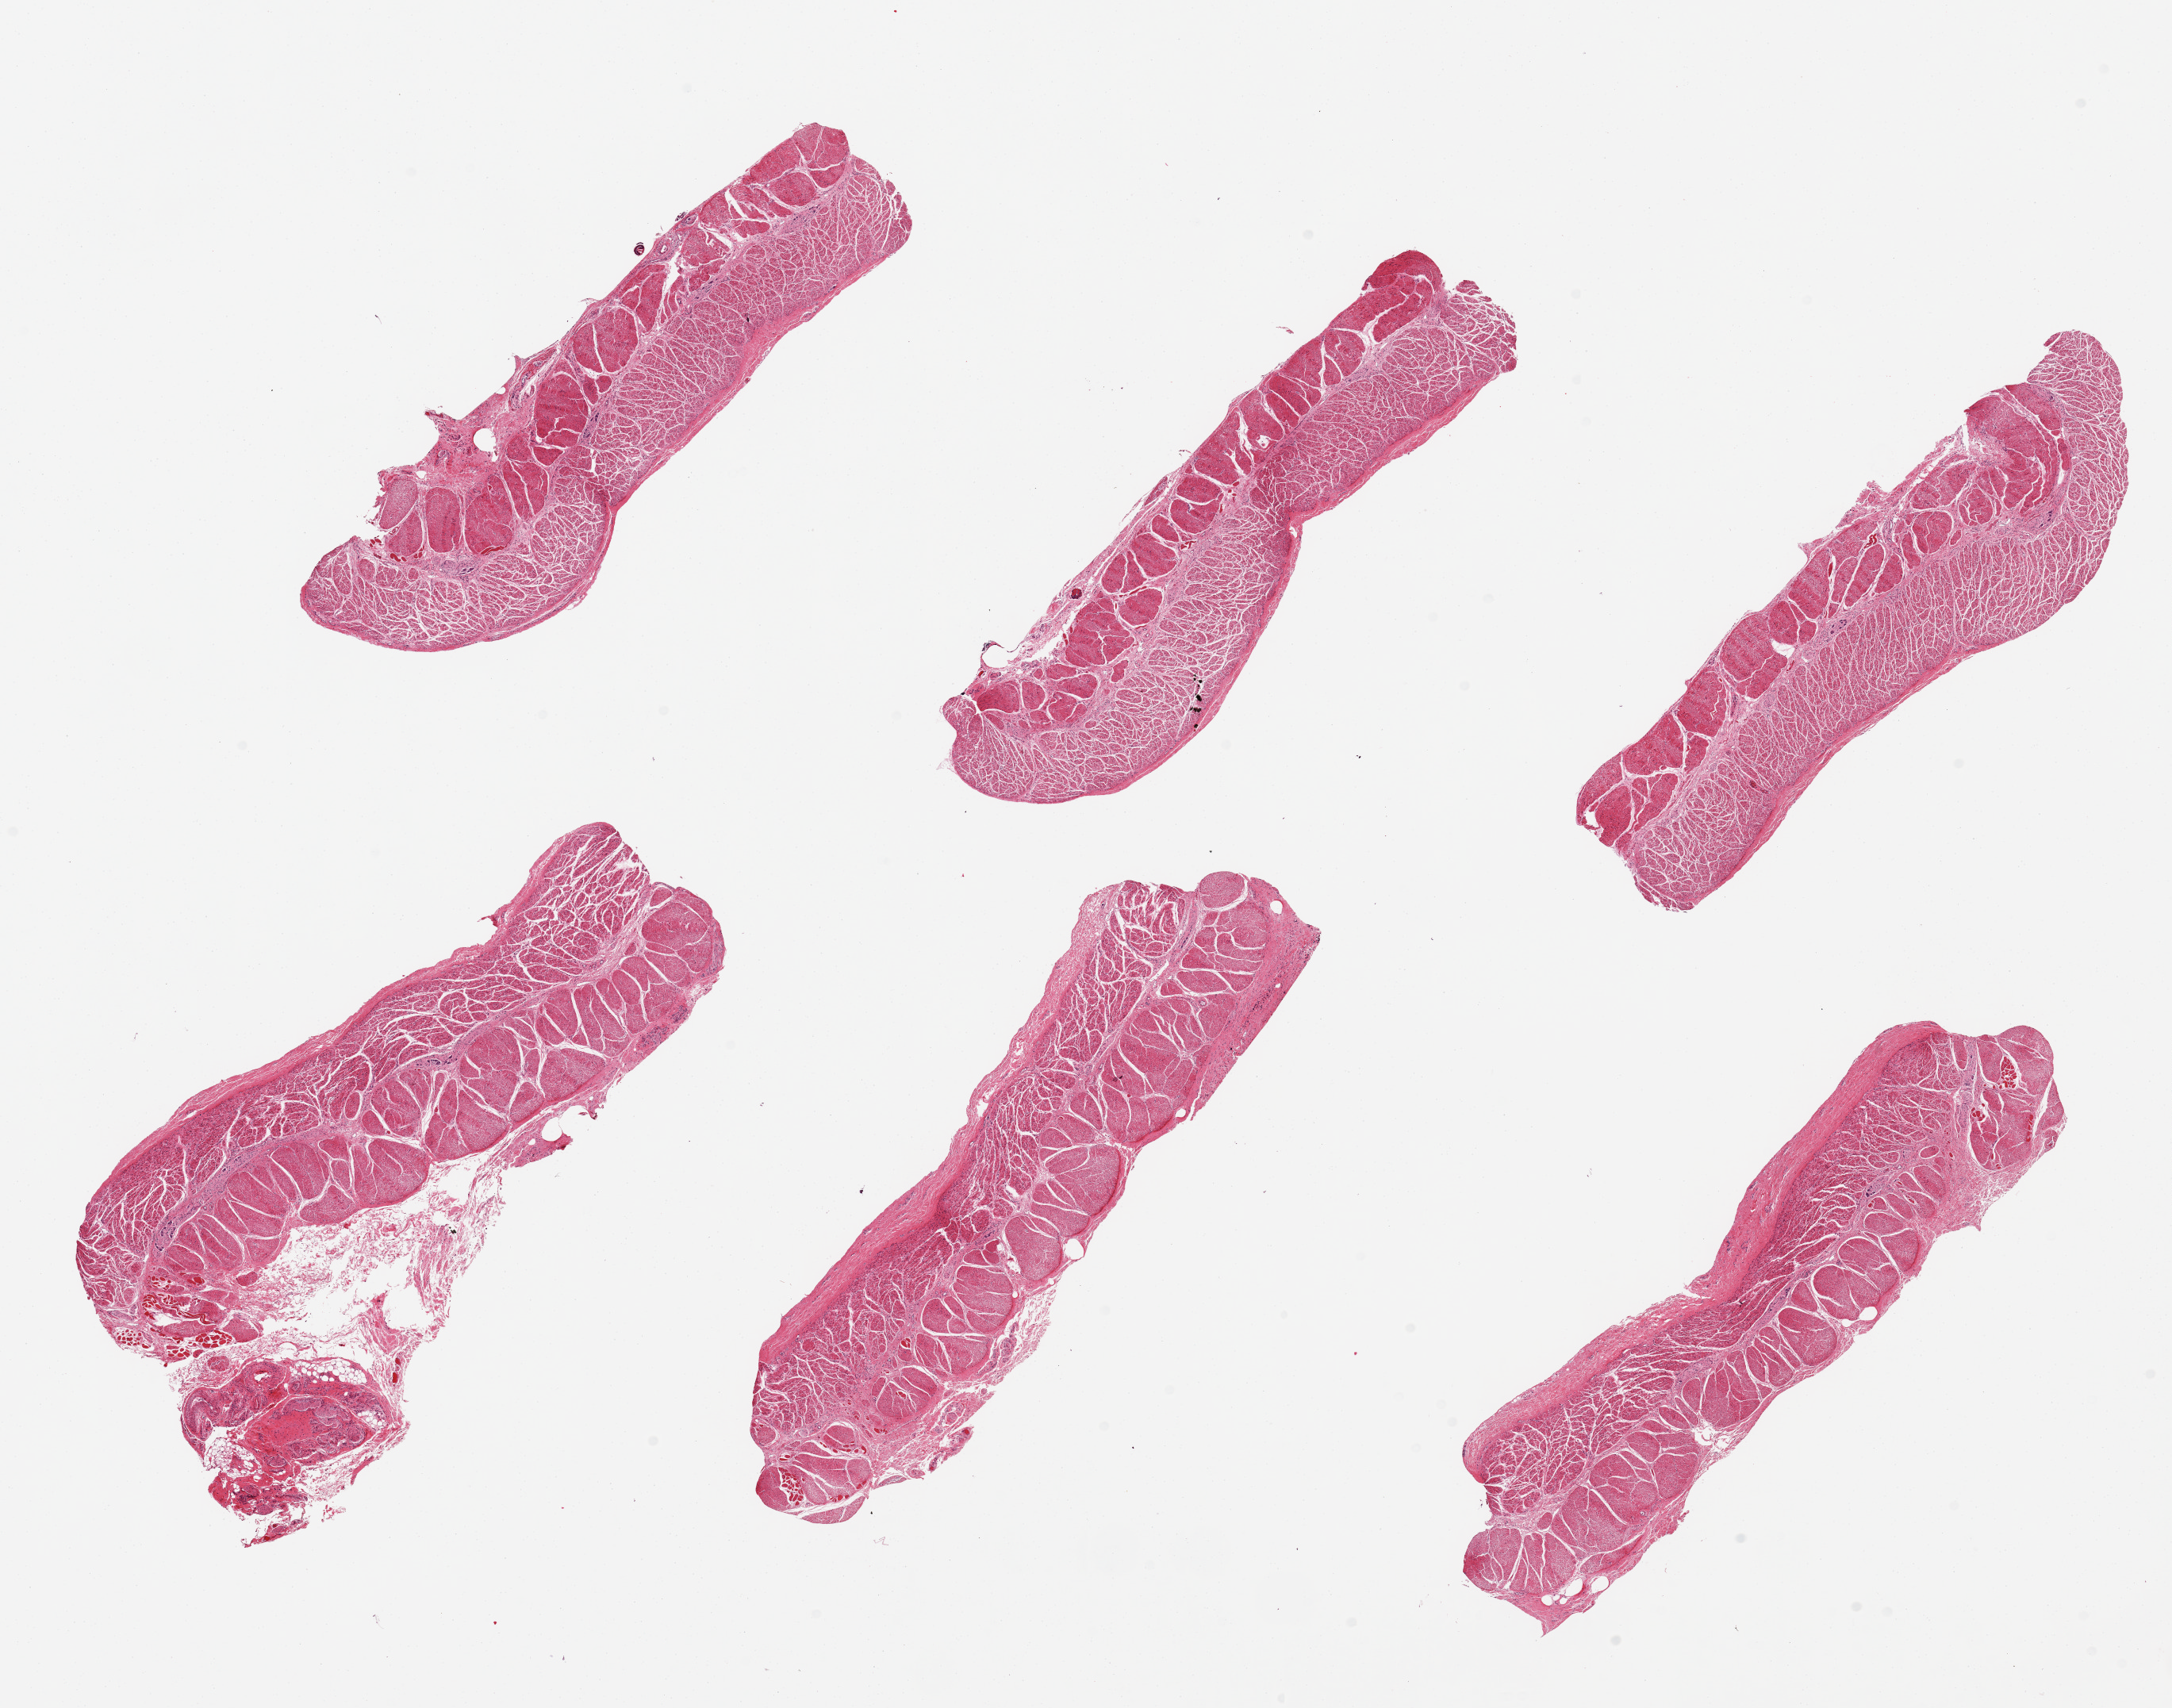
Whole-slide image, H&E stain — shown as a low-resolution overview of the whole scanned area (about 21.7 x 17.0 mm, from a 20x scan); PAXgene-fixed paraffin-embedded (PFPE) section; target tissue: esophageal muscle; tissue donor sample.
Reviewer comment on this tissue sample: 6 pieces, confirmed target muscularis.